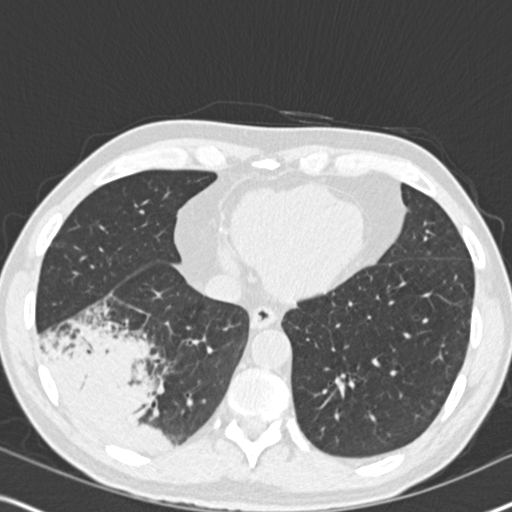
Chest CT (low-dose screening protocol), one axial image, second screening round (one year after baseline), lung window (W 1500 / L -600 HU), standard (soft-tissue) reconstruction kernel (B30f), 120 kVp, slice 119 of 182 in the series. Male, age 61 years at enrolment.
• Expert reader's lesion annotation, bounding box <35,304,185,460> (left, top, right, bottom; pixels).
• Reader record for this screening exam (exam-level; its link to the box is not recorded): non-calcified nodule or mass ≥4 mm, right lower lobe, 90 × 80 mm, soft tissue attenuation, pre-existing on the prior screen: yes; interval growth: yes.